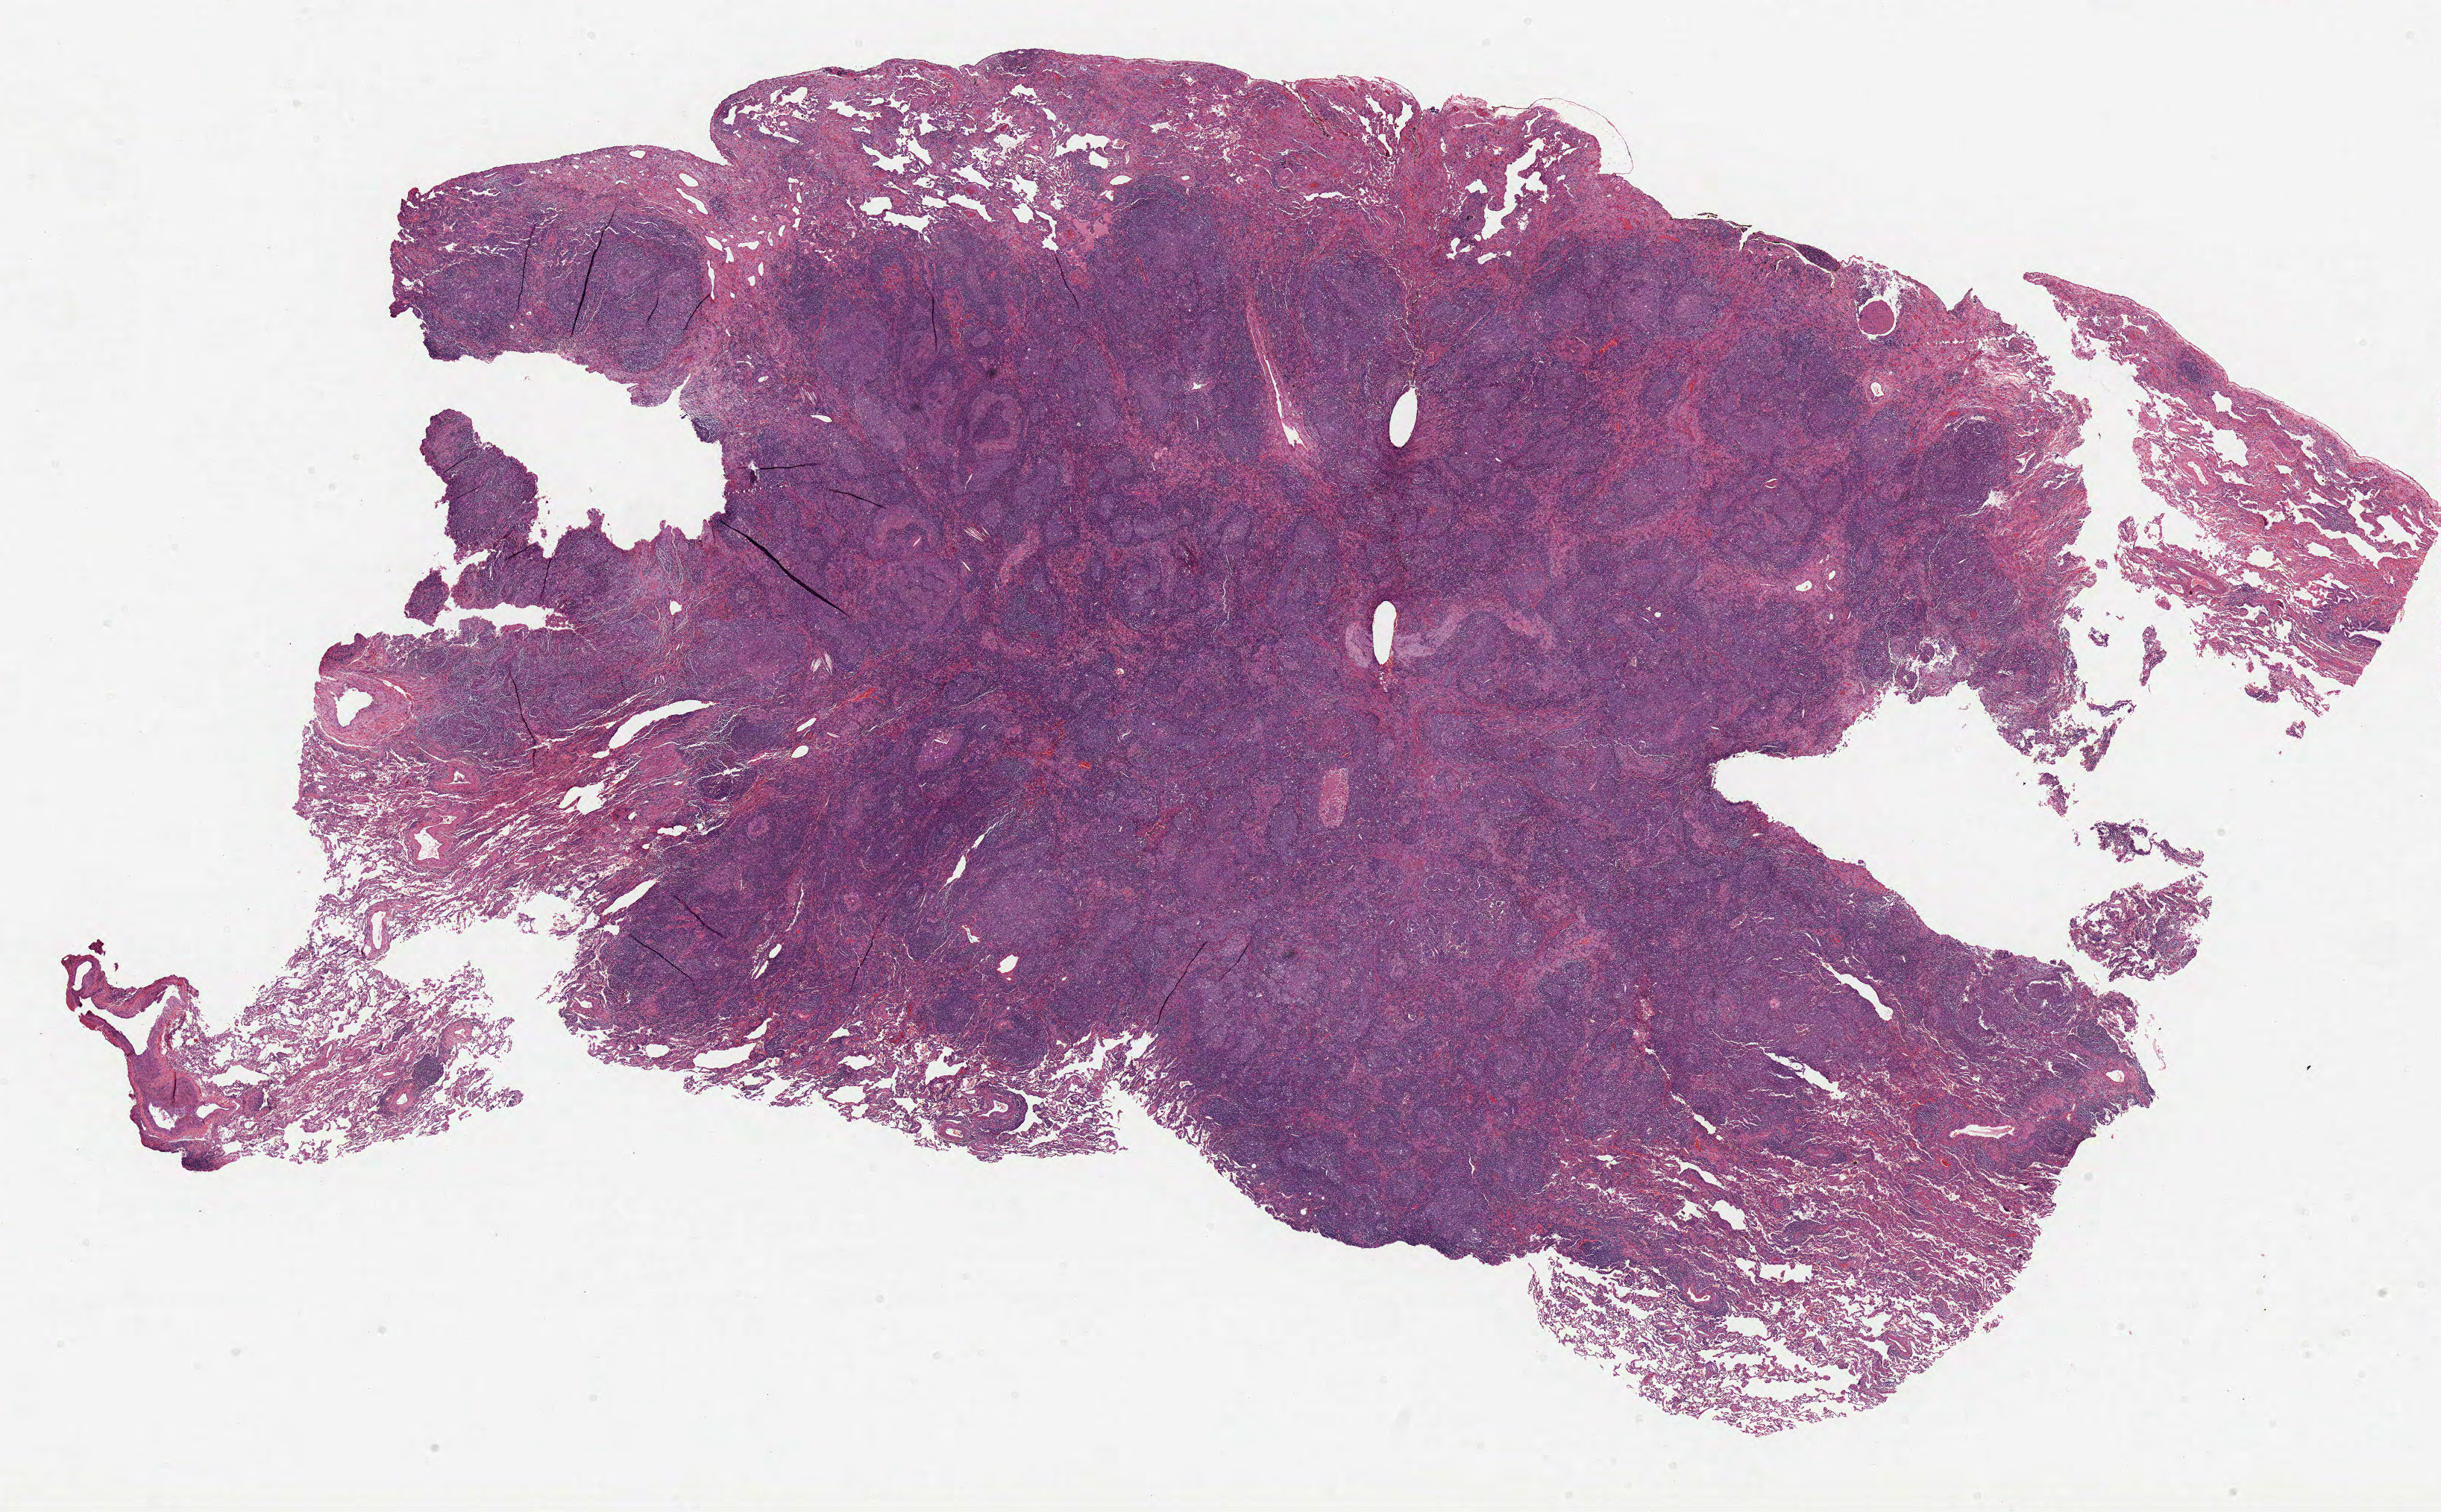
H&E whole-slide image, a low-resolution overview of the entire scanned area, about 26.4 x 16.4 mm. FFPE section. Lung, primary tumour sample. Female, age 81 years at initial diagnosis.
- laterality: left
- histologic diagnosis: Squamous cell carcinoma, NOS (lower lobe, lung)
- AJCC pathologic stage: IIIA
- TNM: T2a N2 M0